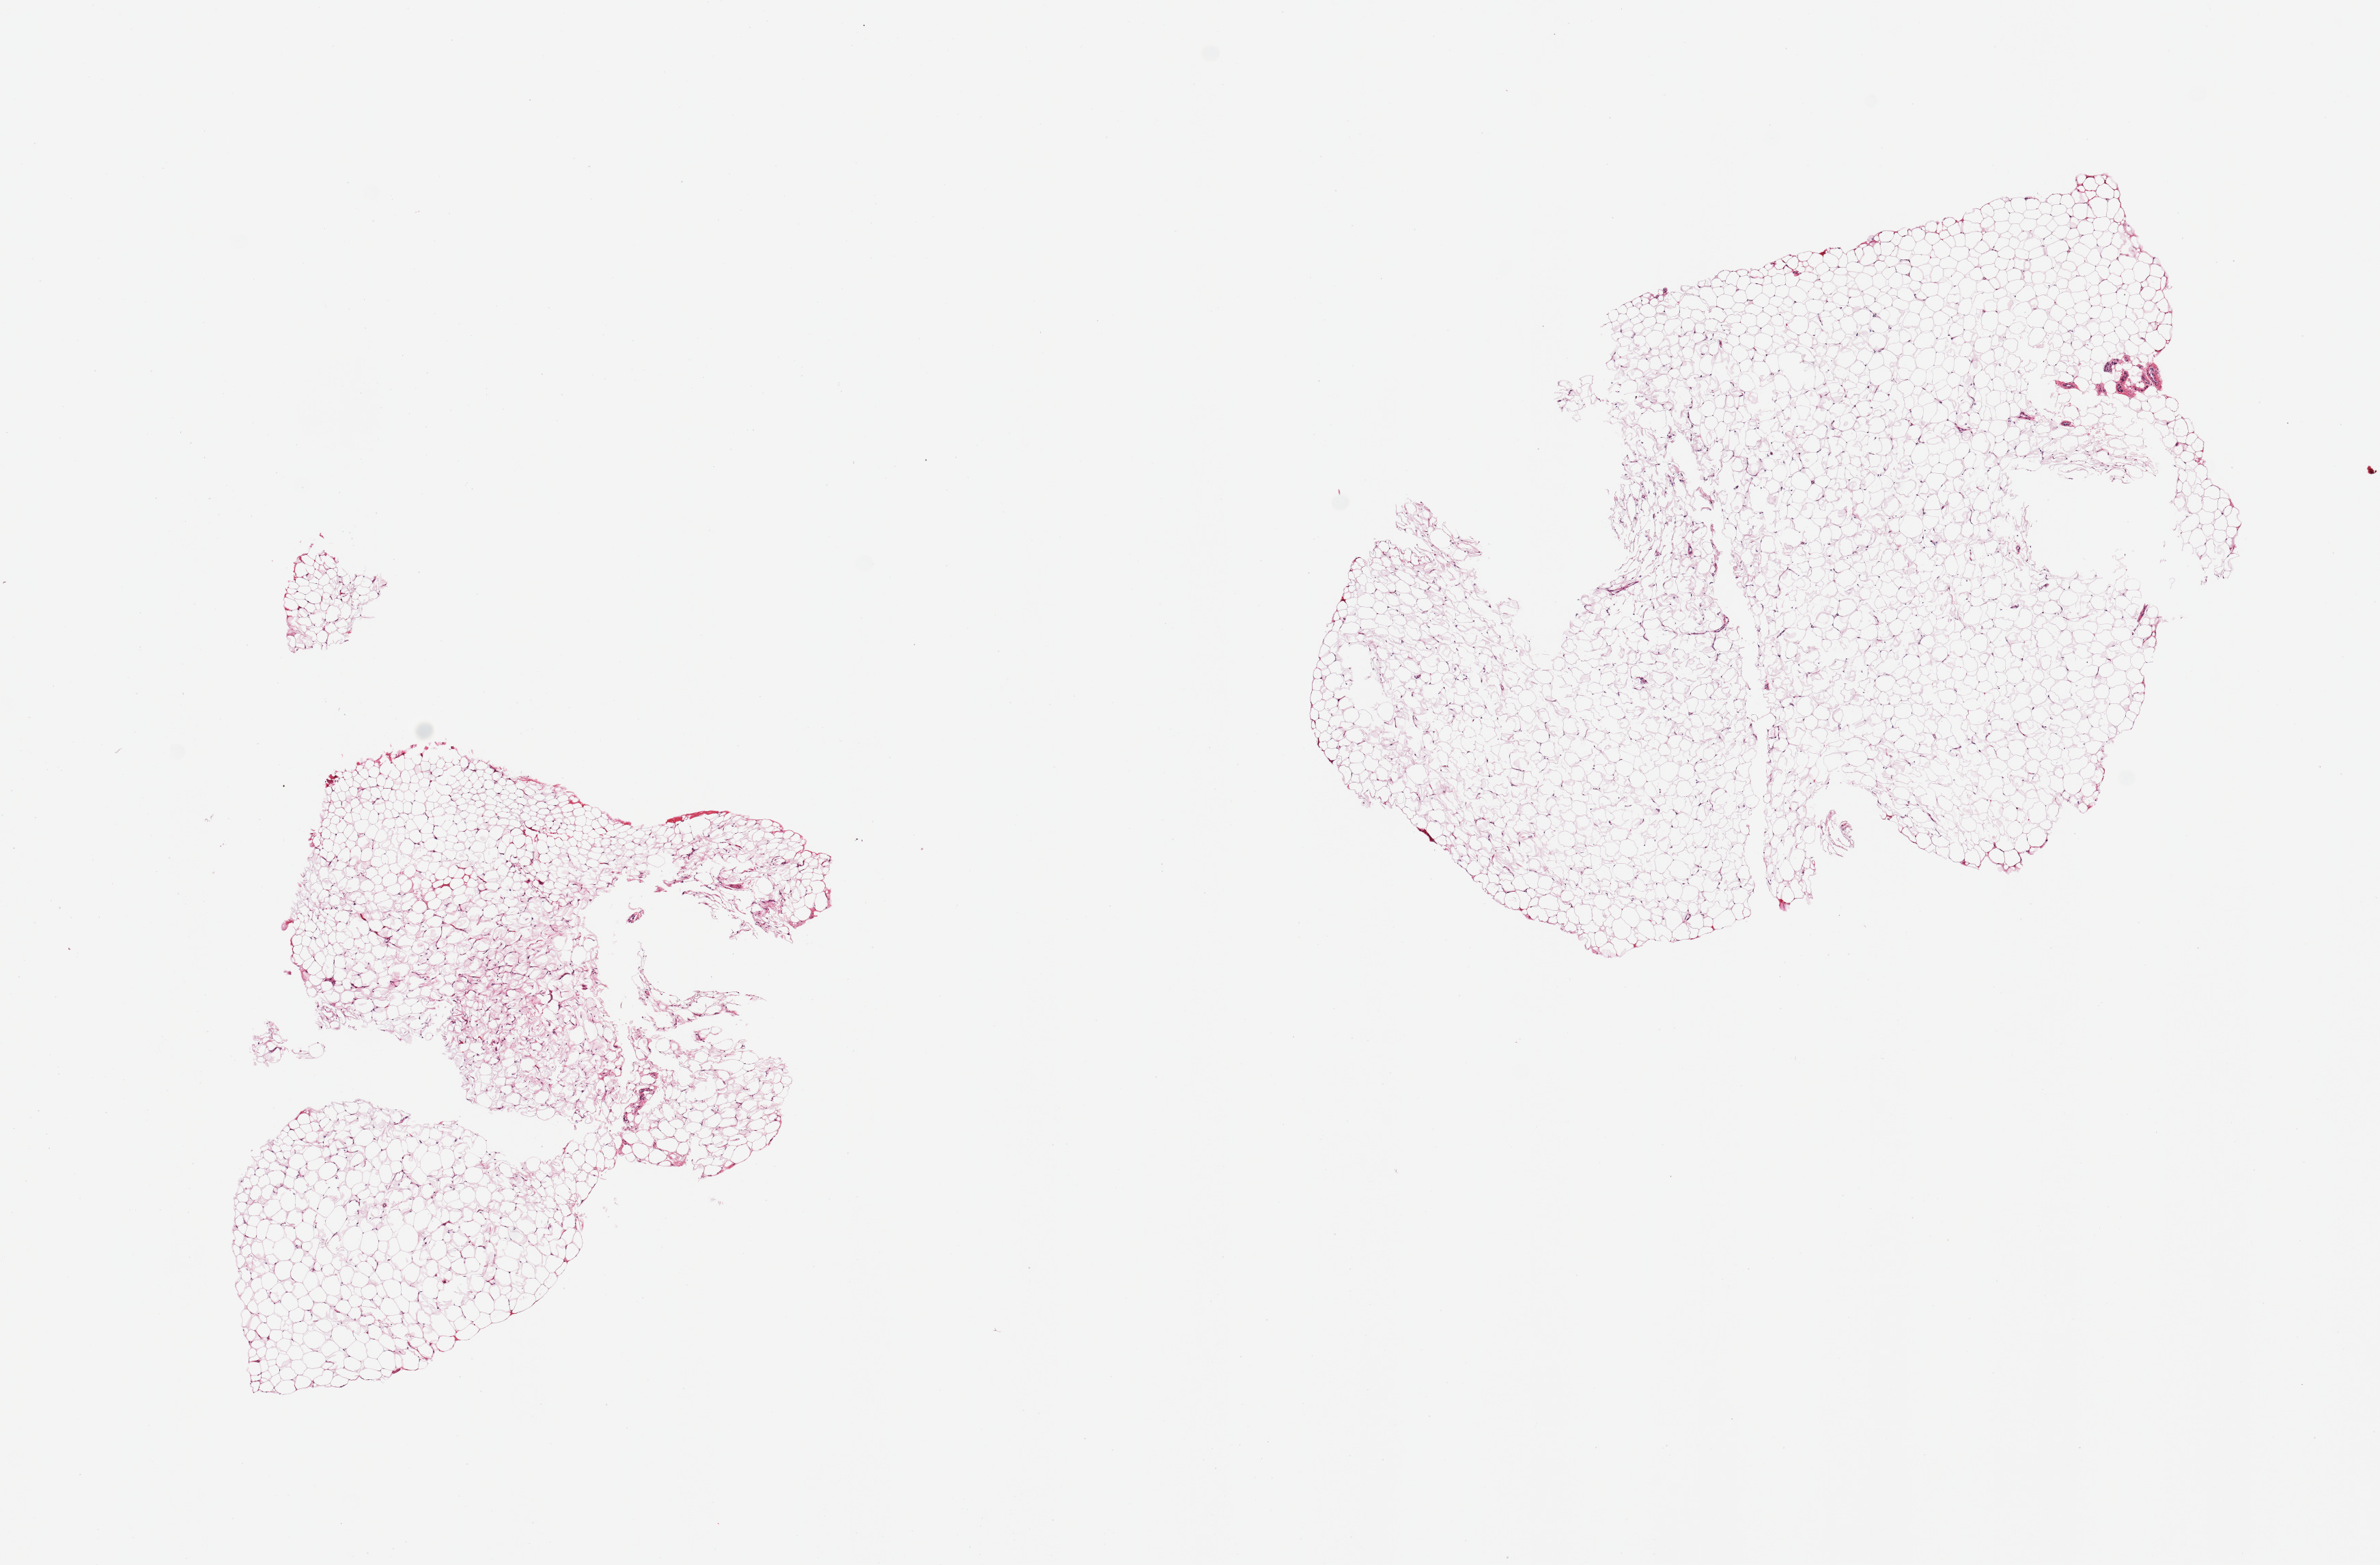
Haematoxylin and eosin whole-slide image, whole scanned area (about 13.8 x 9.1 mm) shown as a low-resolution overview. PAXgene-fixed, paraffin-embedded tissue. Sampled site (target tissue): adipose tissue. Donor tissue sample. Donor: male.
- reviewer comment on this tissue sample: 2 pieces, barely trace fascia